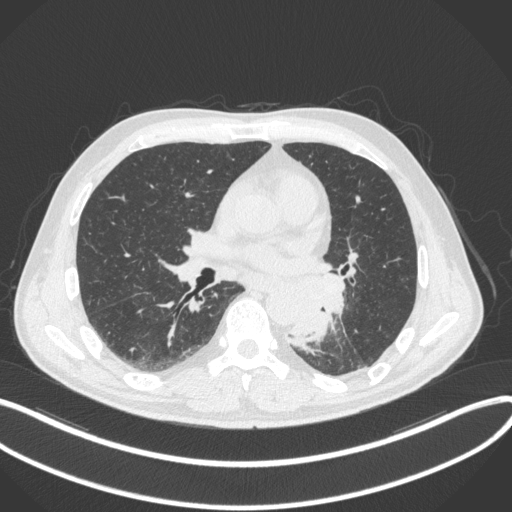
Chest CT, one axial slice. Position 167 of 328 along the scan axis. Reconstruction kernel B31f. 120 kVp. Lung window (W 1500 / L -600 HU). 1 mm slice thickness. 512 × 512 image matrix, field of view 400 × 400 mm. Patient: male, 59 years. Case-level facts recorded for this patient, not image findings: clinical TNM (as recorded): T2a N2 M0.
Structures marked on this image (bounding box drawn by a radiologist):
- lung tumour (recorded histology: squamous cell carcinoma): box from (x=290, y=269) to (x=346, y=349) px